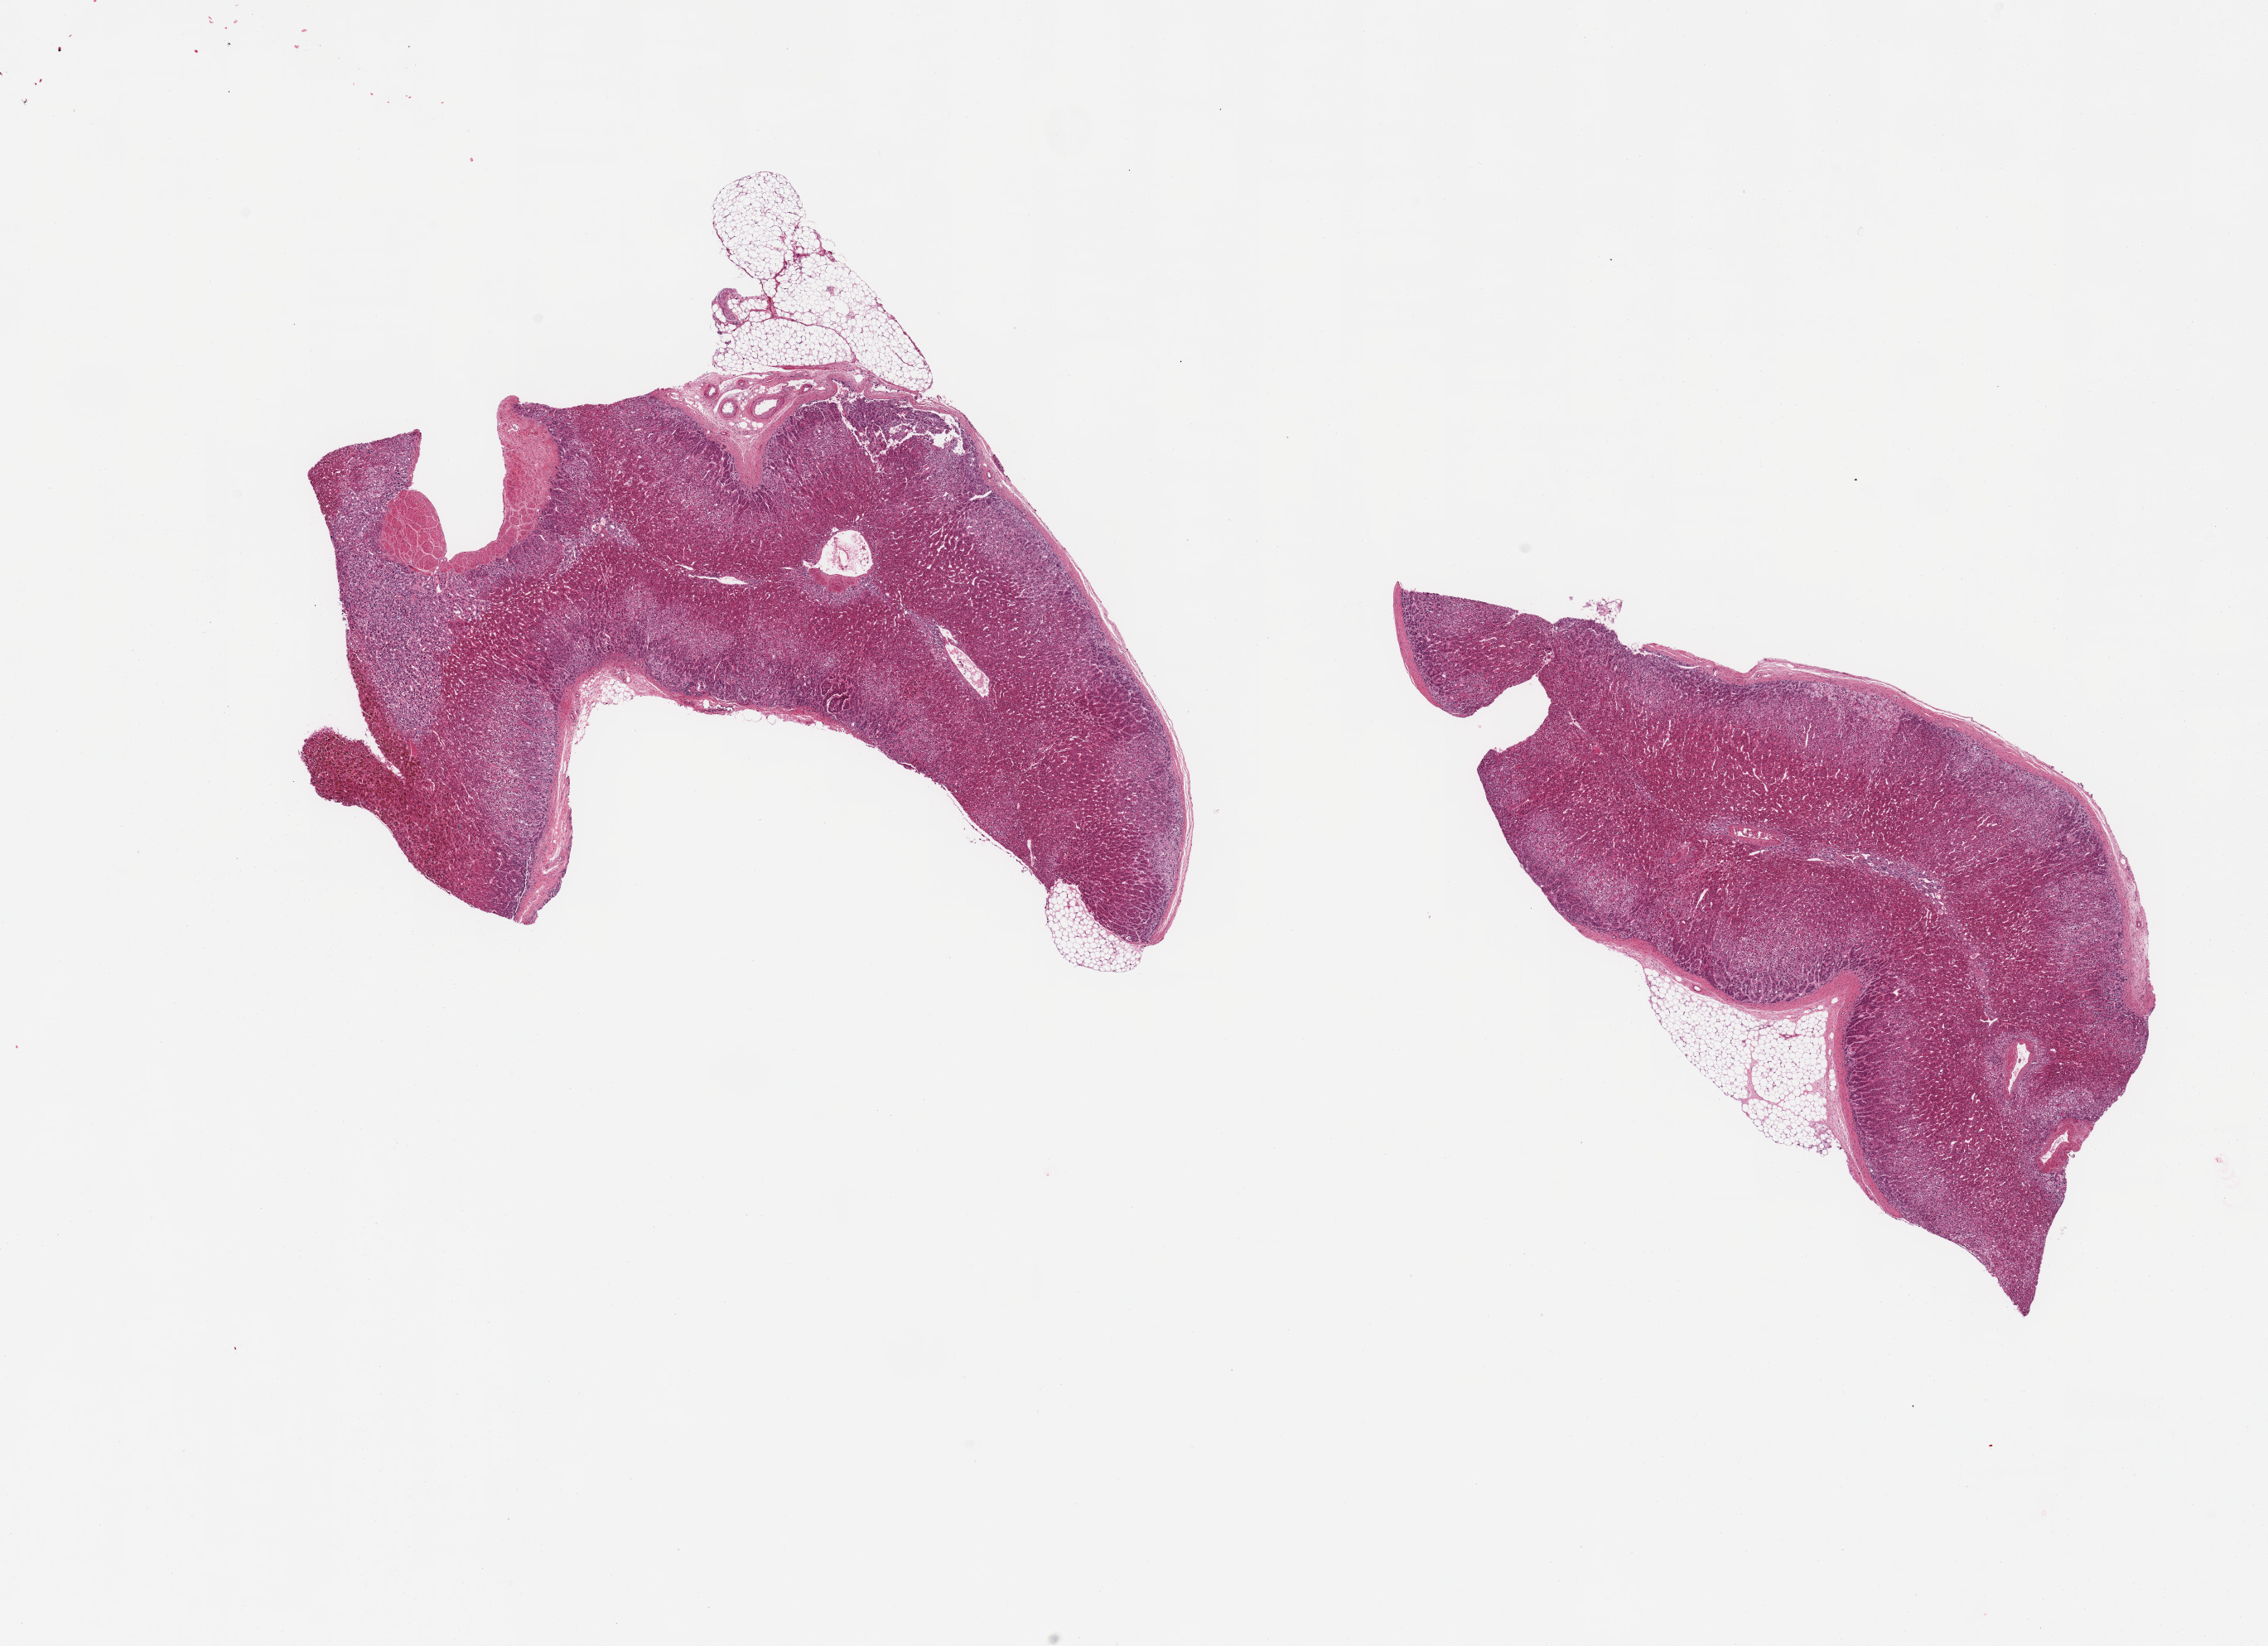
Whole-slide image, haematoxylin and eosin stain, brightfield — shown as a low-resolution overview of the whole scanned area (about 21.7 x 15.7 mm), PAXgene-fixed paraffin-embedded (PFPE) section, section of adrenal gland (target tissue), donor tissue sample. Donor sex: female.
Review note (as recorded): 2 pieces; mildly autolyzed adrenal cortex; ~15% external fat.